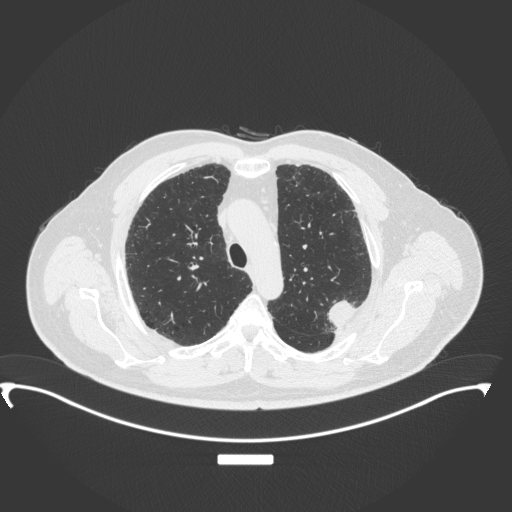
Chest CT, one axial slice; position 268 of 350 along the scan axis; reconstruction kernel B31f; 120 kVp; lung window (W 1500 / L -600 HU); 1 mm slice thickness; 512 × 512 image matrix, field of view 459 × 459 mm. Male patient, age 64 years. From the clinical record (not read from this slice): clinical TNM (as recorded): T1c N1 M1.
Structures marked on this image (rectangle marked by the reading radiologist):
- lung tumour (recorded histology: adenocarcinoma): box from (x=323, y=294) to (x=361, y=336) px